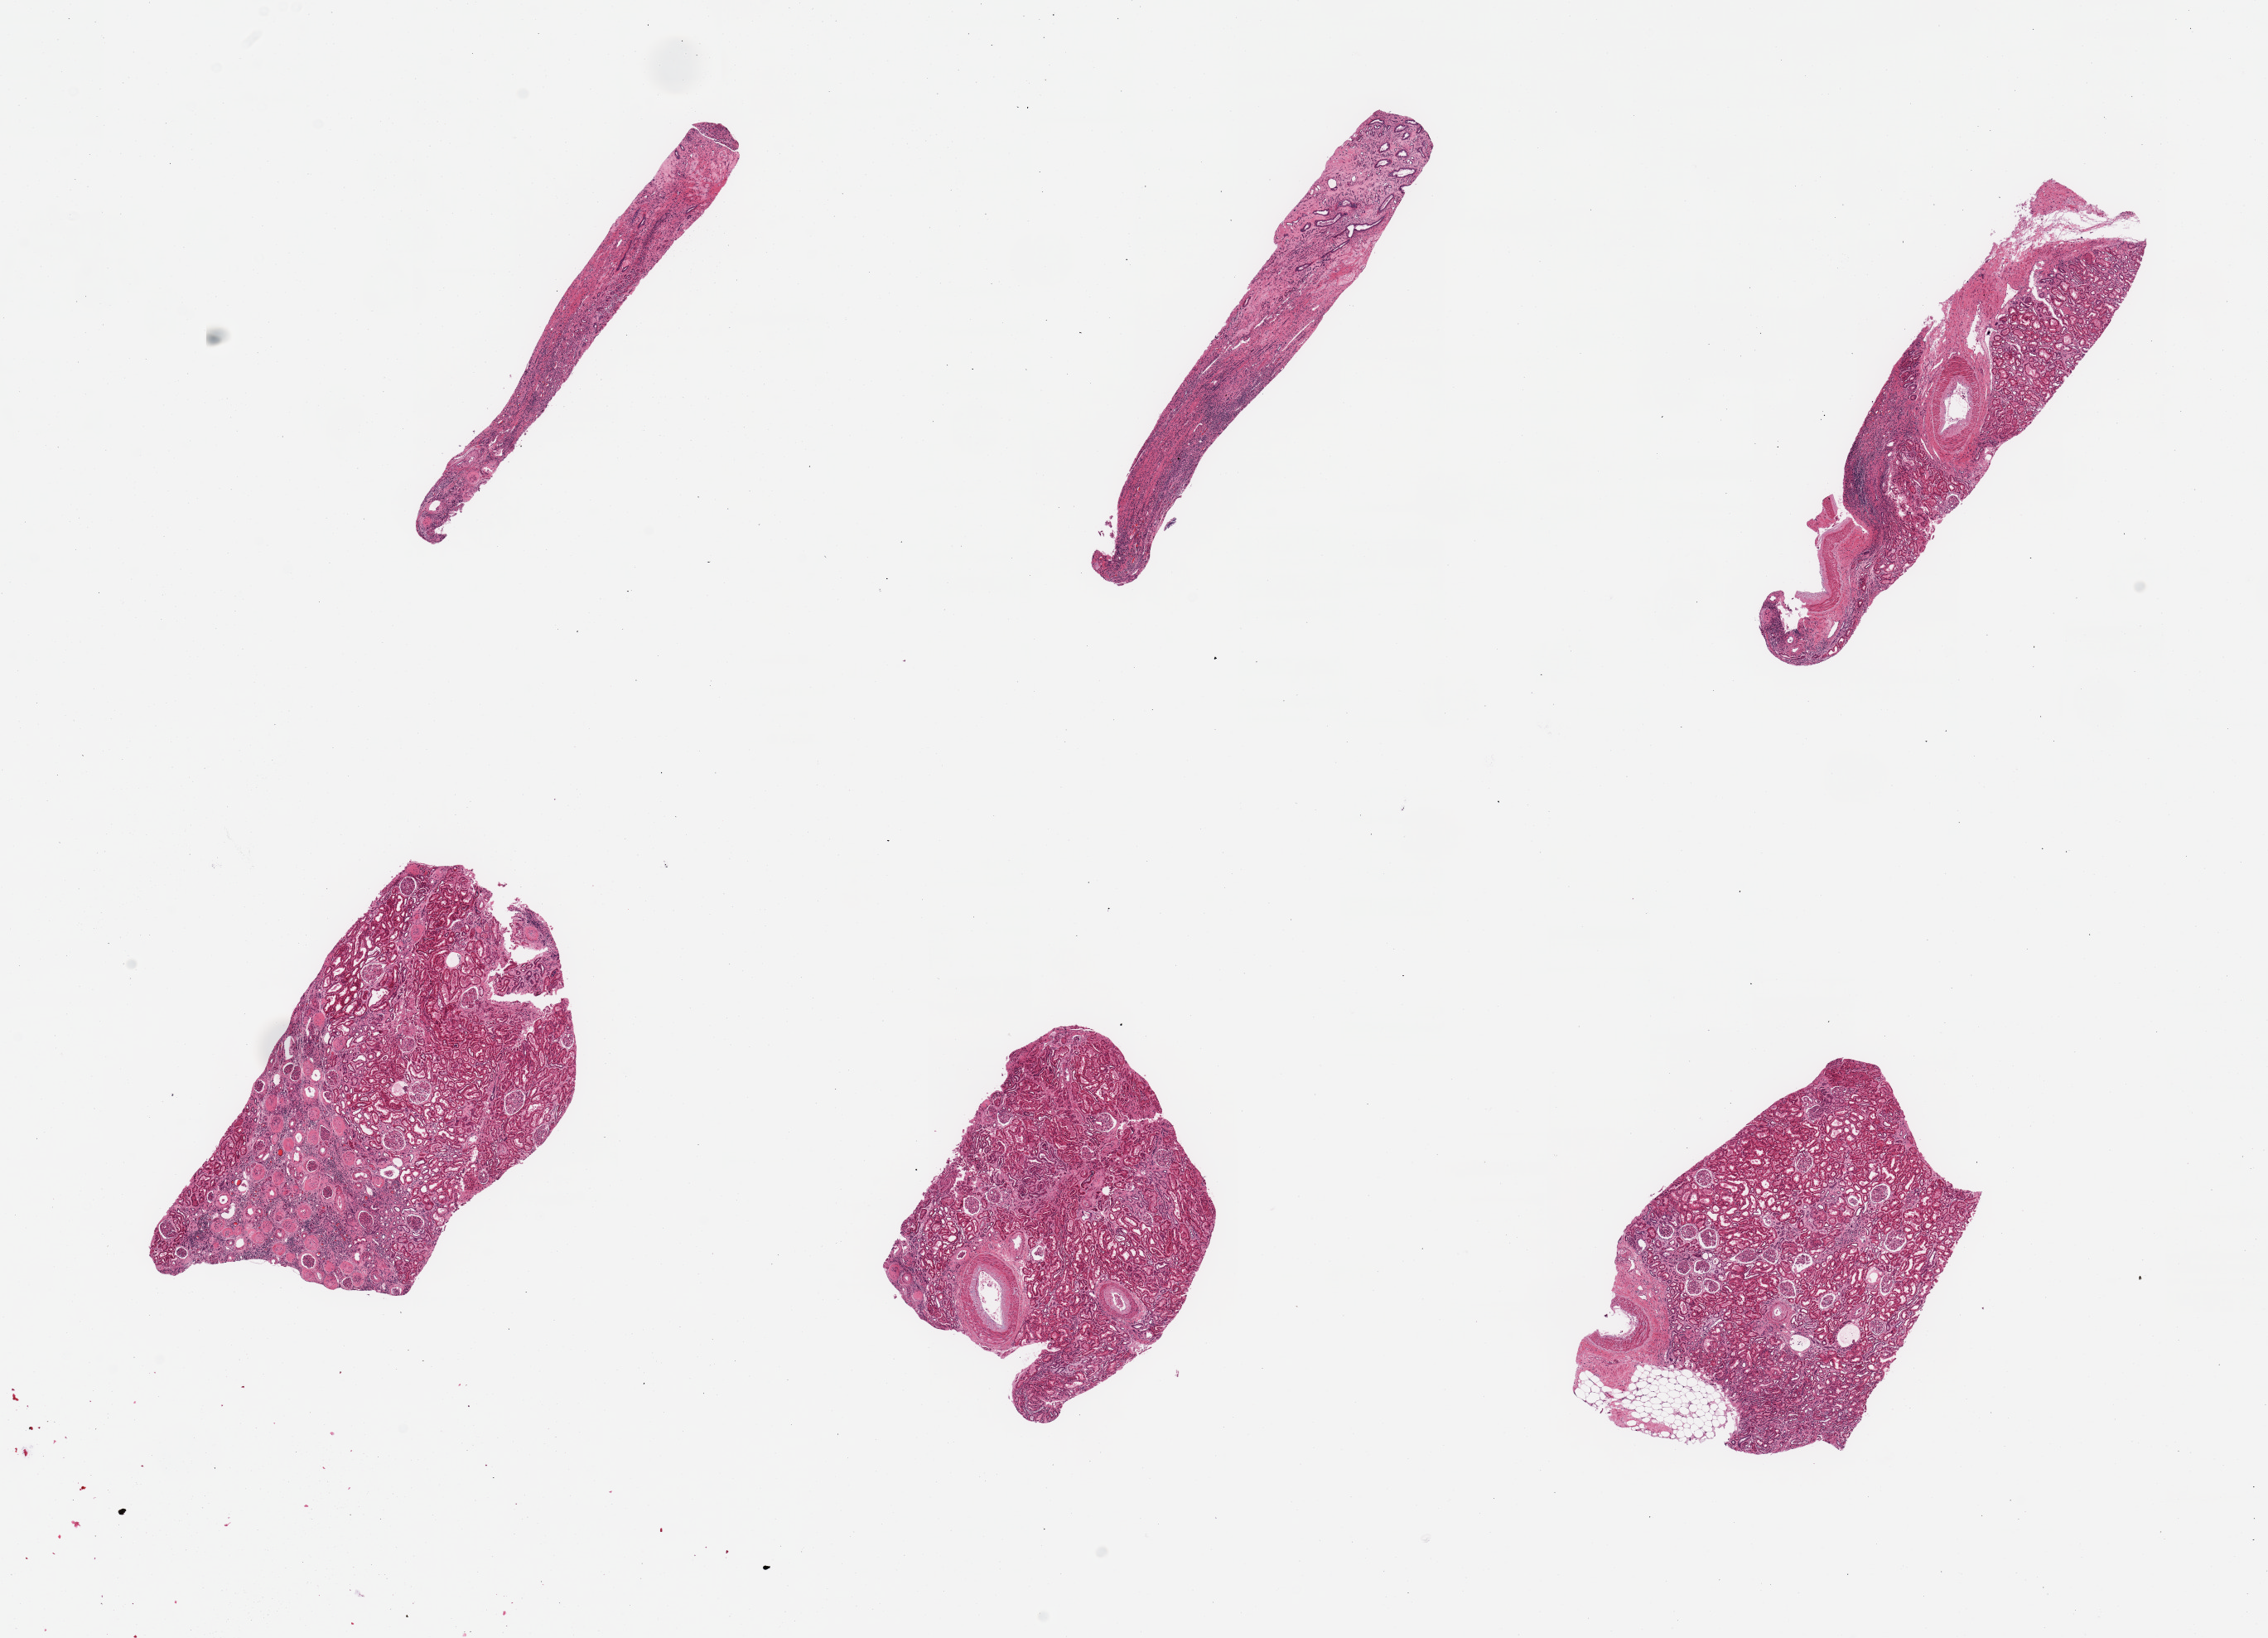
H&E whole-slide image, low-resolution overview of the scanned area, about 21.7 x 15.6 mm; PAXgene-fixed, paraffin-embedded tissue; section of renal cortex (target tissue); tissue donor sample. Donor: female.
Review note (as recorded): 6 pieces; arterio- and arteriolonephrosclerosis; glomerular hyalinization, scarring and interstitial inflammation.